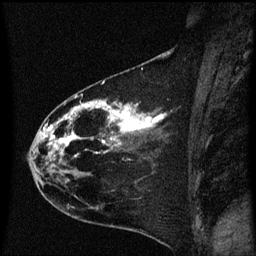
Breast MRI (dynamic contrast-enhanced), one sagittal slice. Slice 27 of 60 in the series (ordered by position). Dynamic contrast-enhanced series, image 2 of 3 at this slice position (ordered by acquisition). 1.5 T. TE 4.2 ms, TR 8.4 ms. 256 × 256 image matrix, field of view 200 × 200 mm. Female patient, age 35 years. Case-level facts recorded for this patient, not image findings: setting: breast cancer imaged before/during neoadjuvant chemotherapy; receptor status: HER2-positive.
Outlined on this slice (semi-automatic segmentation, software-assisted and operator-edited):
- analysis volume of interest (the breast-tissue region the enhancement analysis was run in; not a lesion): bounding box [x1, y1, x2, y2] px = [24, 68, 174, 173]
- tumour enhancement mask (voxels above the 70 % enhancement threshold inside the analysis volume of interest): [37, 102, 165, 171]